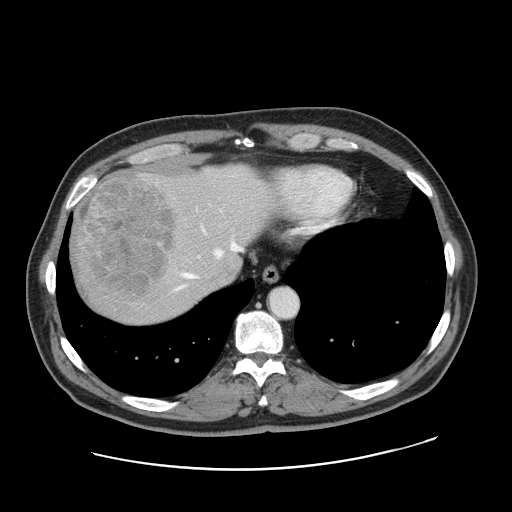
Contrast-enhanced abdominal CT, one axial slice; position 138 of 178 along the scan axis; 120 kVp; intravenous contrast given; soft-tissue window (W 400 / L 40 HU); 2.5 mm slice thickness; 512 × 512 image matrix, field of view 403 × 403 mm. Male patient, age 63 years. Case-level facts recorded for this patient, not image findings: diagnosis: colorectal cancer liver metastases, imaged before liver resection; multiple liver metastases: yes; largest metastasis: 8 cm; chemotherapy before resection: no.
Outlined on this slice (expert manual segmentation):
- hepatic veins: bounding box (x1, y1, x2, y2) in pixels: (175, 228, 243, 291)
- liver: (69, 163, 275, 325)
- planned liver remnant (the part of the liver to remain after resection): (173, 167, 275, 280)
- portal vein (with intrahepatic branches): (159, 242, 162, 244)
- liver metastasis: (71, 169, 177, 297)